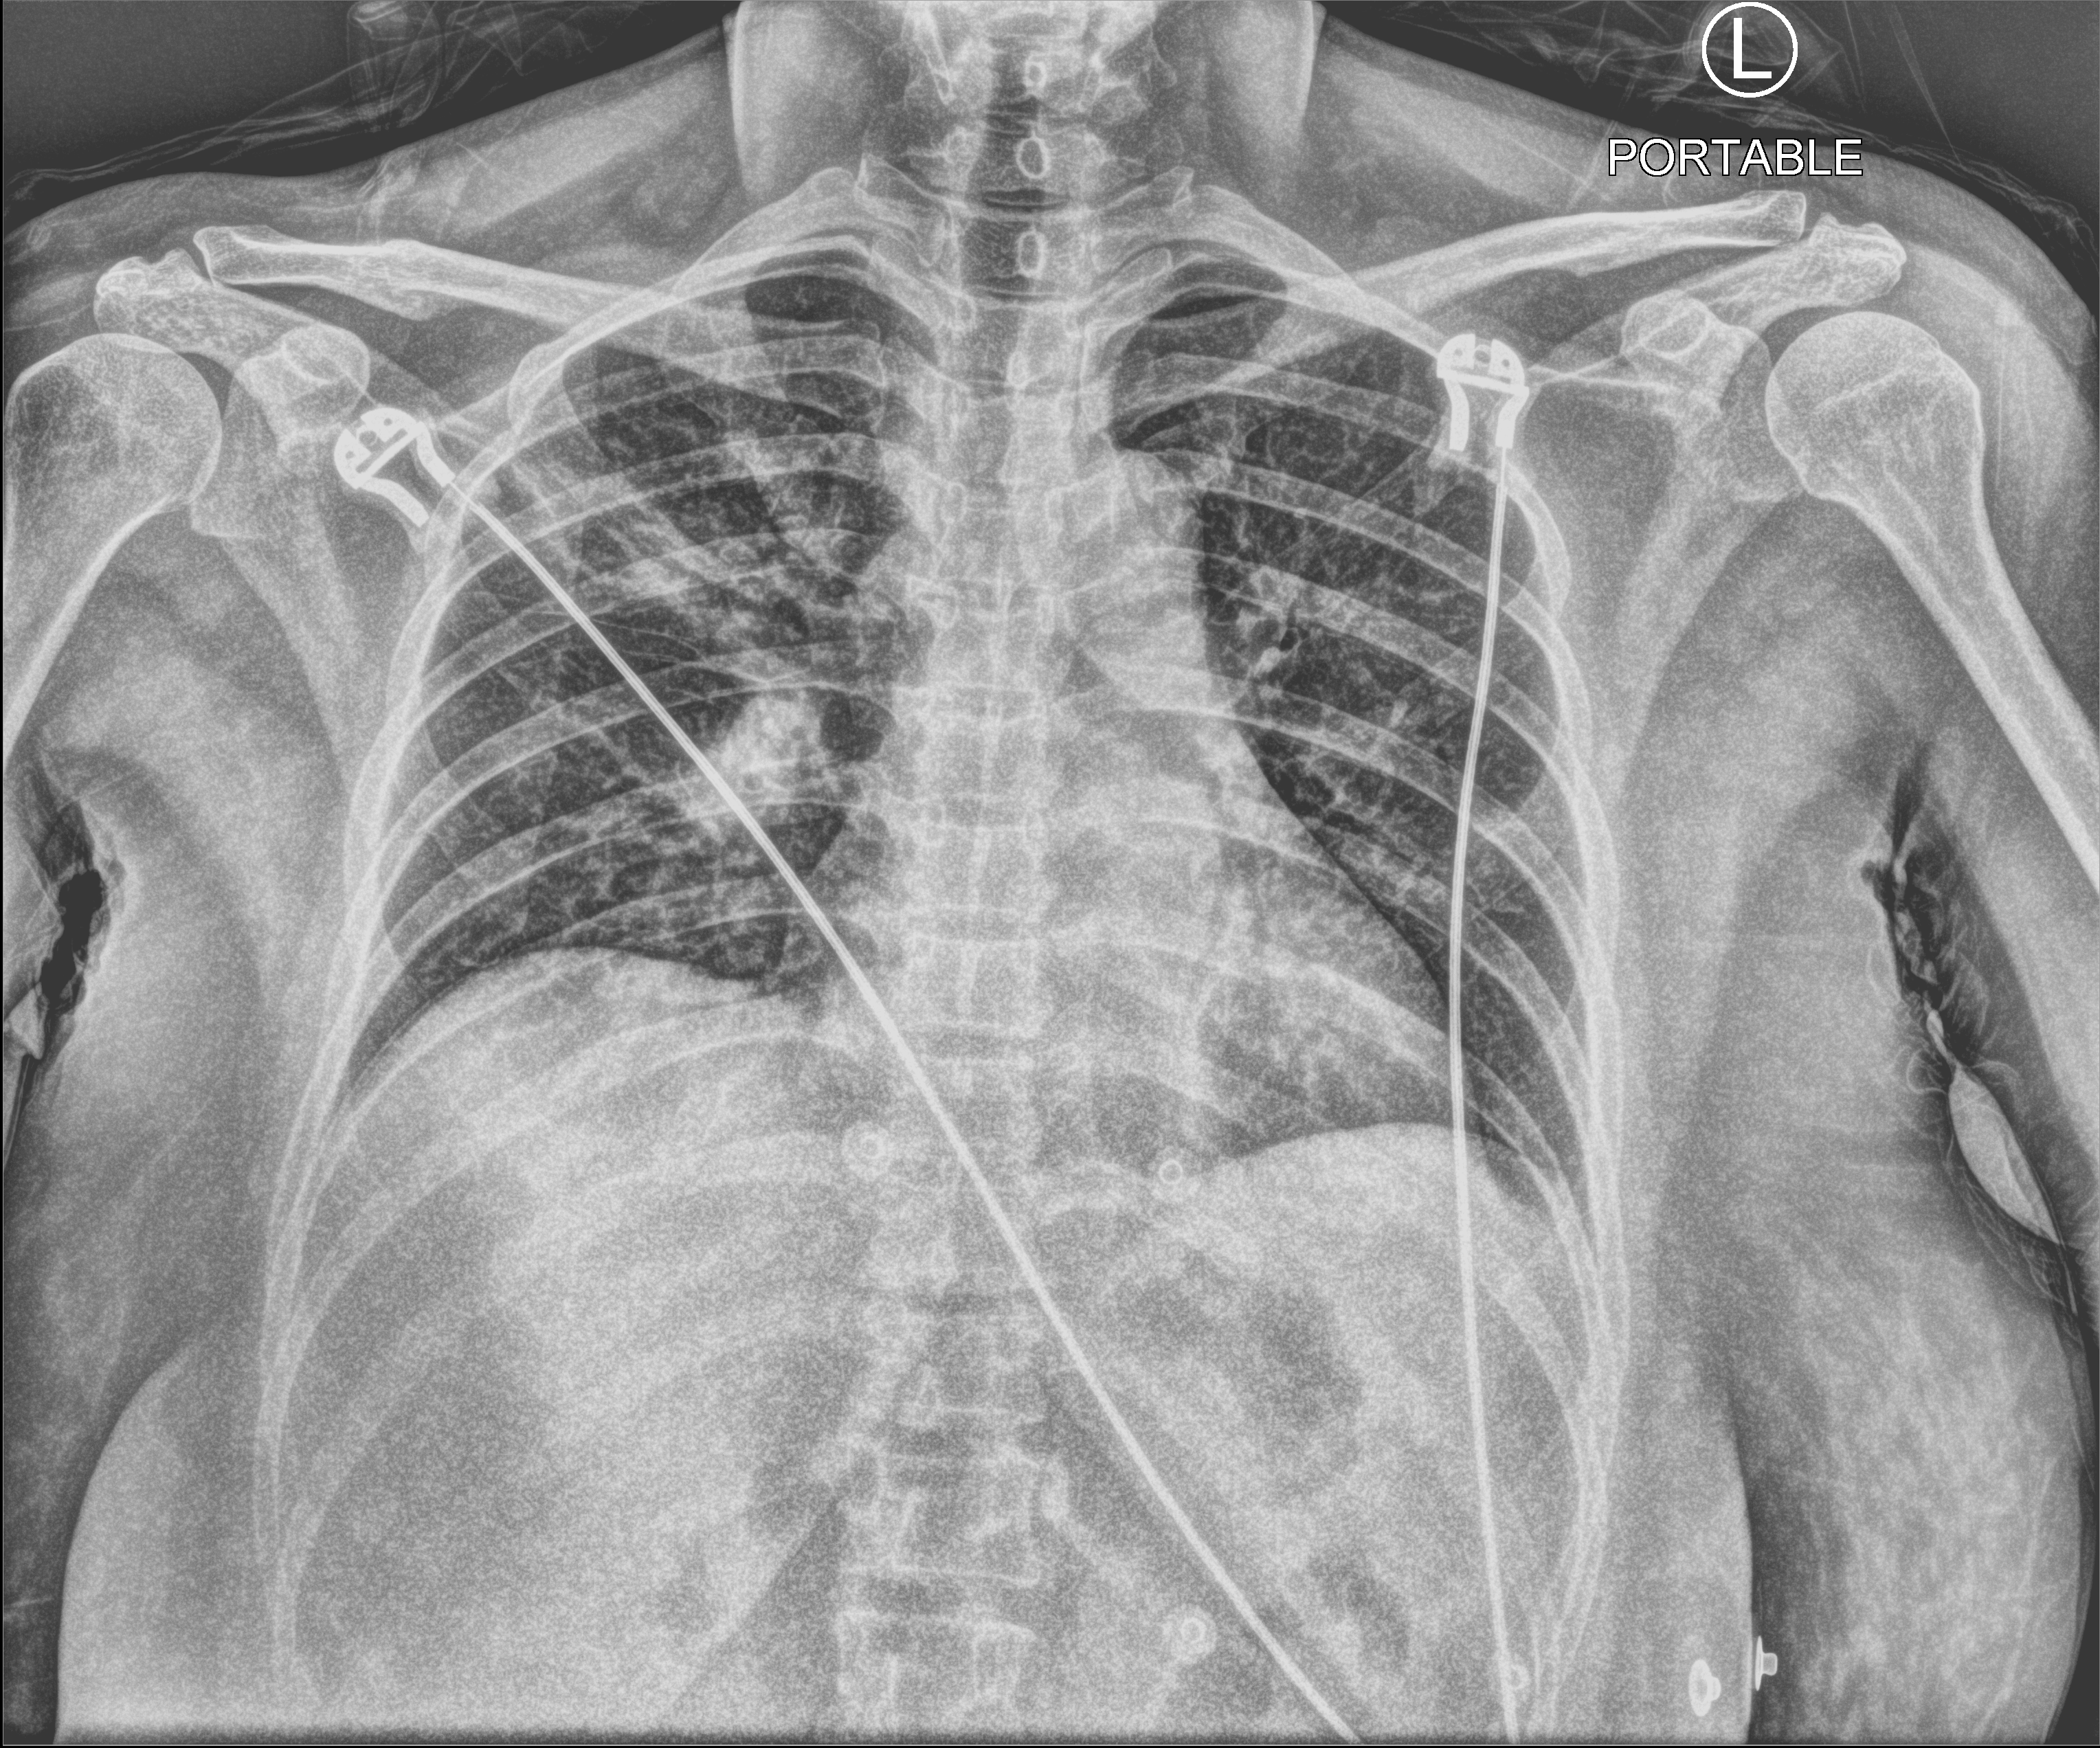
Bedside chest radiograph (computed radiography), anteroposterior (AP) projection. Male patient hospitalised with COVID-19, age 18–59 years.
From the hospital-stay record, not from the radiograph (when in the stay this image was taken is not recorded):
- length of hospital stay: 1 day
- mechanically ventilated during this hospital stay: no
- admitted to intensive care during this hospital stay: no